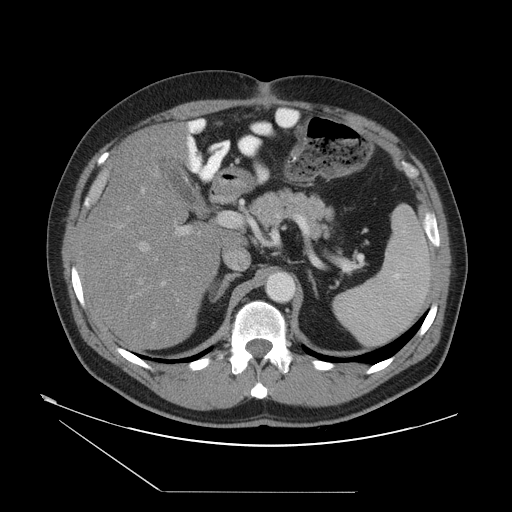
Contrast-enhanced abdominal CT, one axial slice; position 29 of 55 along the scan axis; reconstruction kernel STANDARD; intravenous contrast given; soft-tissue window (W 400 / L 40 HU); 5 mm slice thickness; 512 × 512 image matrix. Male patient, age 59 years. Case-level facts recorded for this patient, not image findings: diagnosis: colorectal cancer liver metastases, imaged before liver resection; multiple liver metastases: yes.
Annotated regions visible in this slice (manually delineated by an expert):
- hepatic veins: bounding box (x1, y1, x2, y2) in pixels: (138, 135, 200, 328)
- liver: (84, 125, 229, 350)
- planned liver remnant (the part of the liver to remain after resection): (84, 136, 229, 350)
- portal vein (with intrahepatic branches): (160, 223, 200, 302)